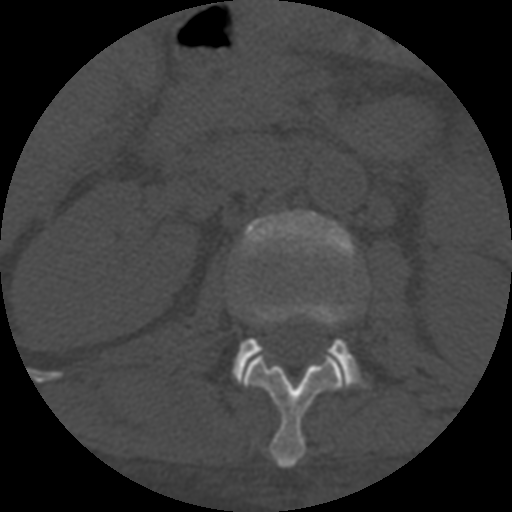
CT including the spine, one axial slice. Position 274 of 708 along the scan axis. One of 3 acquisitions stored at this slice position. Bone window (W 1800 / L 400 HU). 1.25 mm slice thickness. 512 × 512 image matrix, field of view 160 × 160 mm. Patient age 55 years. From the clinical record (not read from this slice): primary cancer: colon; vertebrae with lytic lesions (as recorded): T12, L1, L5.
Outlined on this slice (semi-automatic segmentation, software-assisted and operator-edited):
- L1 vertebra: bounding box [x1, y1, x2, y2] px = [241, 319, 346, 467]
- L2 vertebra: [233, 210, 360, 385]